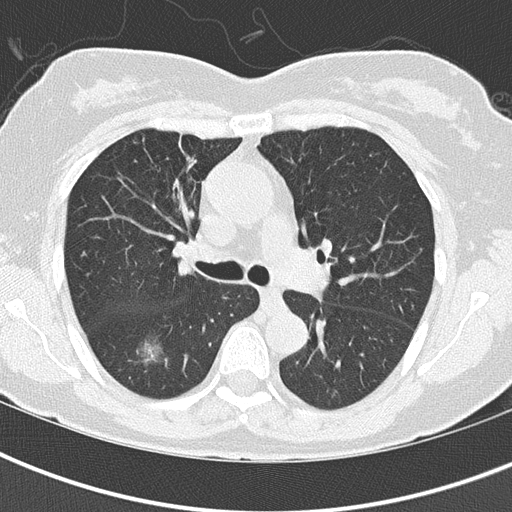
Low-dose screening chest CT, axial slice, first (baseline) screen, lung window (W 1500 / L -600 HU), 2 mm slice thickness, lung (sharp) reconstruction kernel (B50f), slice 65 of 200 in the series. Female, age 68 years at enrolment. Former smoker at enrolment.
Expert reader's lesion annotation, bounding box [x1, y1, x2, y2] px = [121, 326, 179, 377]. The exam's reader record, not a measurement of the box and not confirmed to be the same lesion: non-calcified nodule or mass ≥4 mm, right lower lobe, 19 × 17 mm, spiculated (stellate) margins, ground glass attenuation. Official screen result: positive, change unspecified: nodule(s) >= 4 mm or enlarging nodule(s), mass(es), or other non-specific abnormalities suspicious for lung cancer. Later outcome: lung cancer diagnosed 40 days after this screen — bronchiolo-alveolar adenocarcinoma, NOS, right lower lobe, well differentiated (G1), stage IA (AJCC 6th edition), 15 mm at pathology.